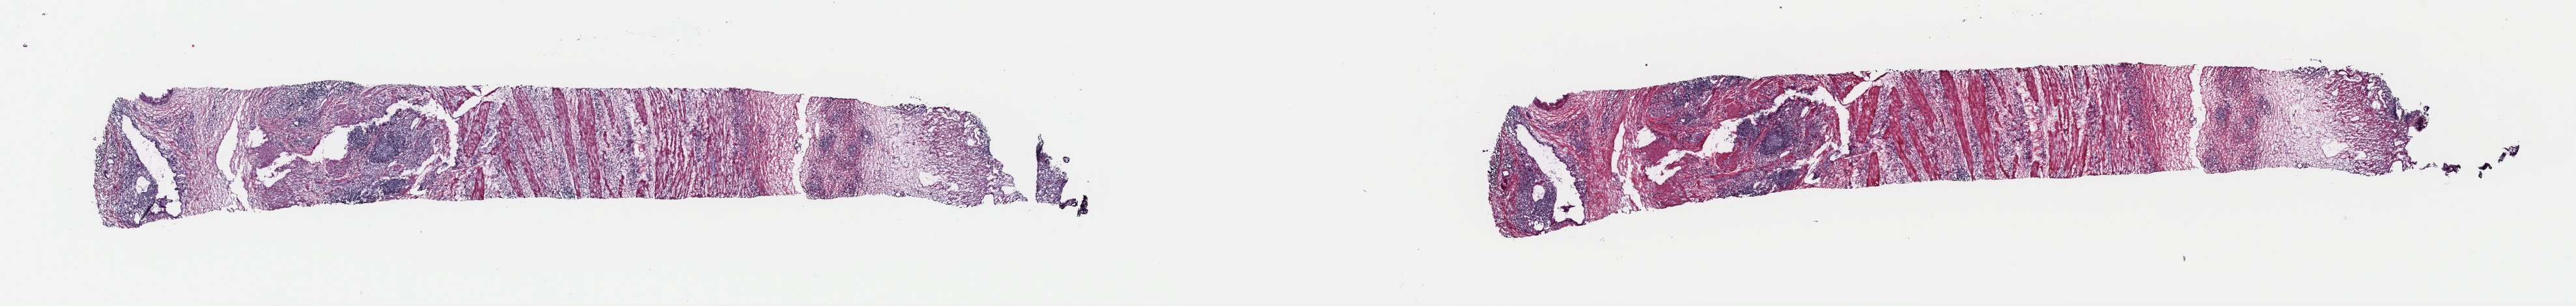
Whole-slide histology image, Hematoxylin and eosin (H&E) stained, a low-resolution overview of the entire scanned area, about 31.2 x 3.7 mm. Frozen section. Primary tumour sample from the stomach. Female patient; age at initial diagnosis 53 years. Composition of this section per pathologist review: tumour cells 35%, tumour nuclei 60%.
Pathologic diagnosis: Carcinoma, diffuse type.